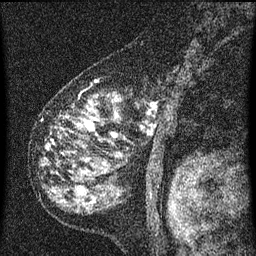
Breast MRI (dynamic contrast-enhanced), one sagittal slice. Position 40 of 60 along the scan axis. Dynamic contrast-enhanced series, image 2 of 3 at this slice position (ordered by acquisition). 1.5 T. TE 4.2 ms, TR 8 ms. 2 mm slice thickness. 256 × 256 image matrix, field of view 180 × 180 mm. Female patient, age 55 years.
Annotated regions visible in this slice (semi-automatic segmentation, software-assisted and operator-edited):
- analysis volume of interest (the breast-tissue region the enhancement analysis was run in; not a lesion): bounding box [x1, y1, x2, y2] px = [42, 76, 185, 155]
- tumour enhancement mask (voxels above the 70 % enhancement threshold inside the analysis volume of interest): [87, 118, 116, 137]